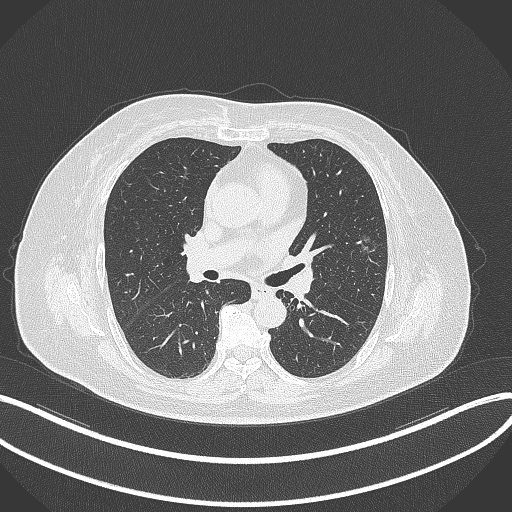
Chest CT, one axial slice; position 202 of 315 along the scan axis; reconstruction kernel B70f; 120 kVp; lung window (W 1500 / L -600 HU); 1 mm slice thickness; 512 × 512 image matrix, field of view 400 × 400 mm. Female patient, age 76 years. Case-level facts recorded for this patient, not image findings: clinical TNM (as recorded): T1b N0 M0.
Annotated regions visible in this slice (bounding box drawn by a radiologist):
- lung tumour (recorded histology: adenocarcinoma): bounding box [x1, y1, x2, y2] px = [355, 225, 380, 257]